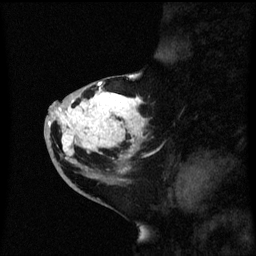
Breast MRI (dynamic contrast-enhanced), one sagittal slice. Position 27 of 60 along the scan axis. Dynamic contrast-enhanced series, image 2 of 3 at this slice position (ordered by acquisition). 1.5 T. TE 4.2 ms, TR 8.4 ms. 2.3 mm slice thickness. 256 × 256 image matrix, field of view 200 × 200 mm. Patient: female, 46 years. Case-level facts recorded for this patient, not image findings: setting: breast cancer imaged before/during neoadjuvant chemotherapy; receptor status: HER2-positive.
Annotated regions visible in this slice (semi-automatically segmented with operator editing):
- analysis volume of interest (the breast-tissue region the enhancement analysis was run in; not a lesion): bounding box <44,86,151,171> (left, top, right, bottom; pixels)
- tumour enhancement mask (voxels above the 70 % enhancement threshold inside the analysis volume of interest): <48,90,145,171>